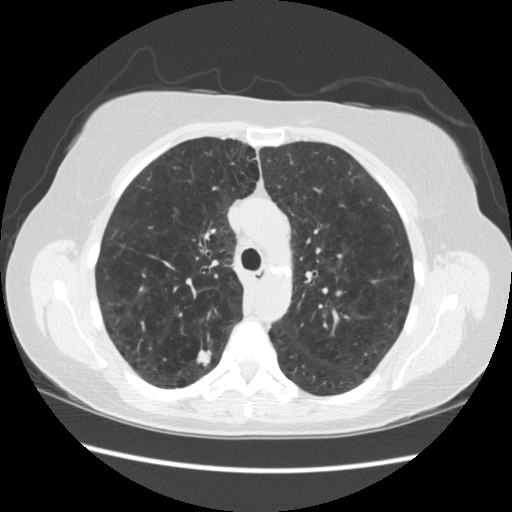
Low-dose screening chest CT, one axial slice. Reconstruction kernel STANDARD. Lung window (W 1500 / L -600 HU). 2.5 mm slice thickness. 512 × 512 image matrix, field of view 360 × 360 mm.
Annotated regions visible in this slice (manually delineated by an expert):
- lesion 1 (tumor, upper lobe of right lung): box from (x=196, y=348) to (x=212, y=368) px